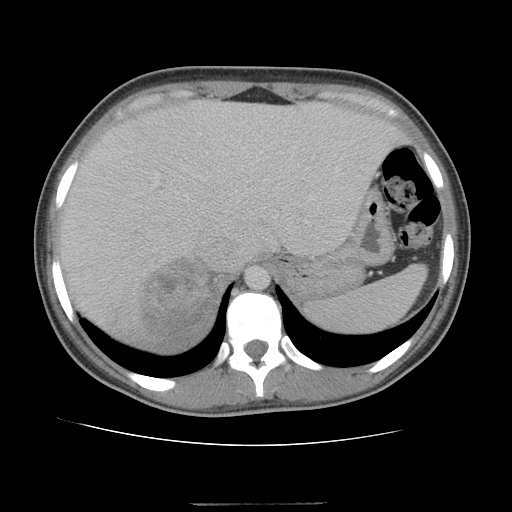
Contrast-enhanced abdominal CT, one axial slice. Slice 83 of 100 in the series (ordered by position). Reconstruction kernel STANDARD. Intravenous contrast given. Soft-tissue window (W 400 / L 40 HU). 5 mm slice thickness. 512 × 512 image matrix, field of view 360 × 360 mm. Female patient, age 21 years. Case-level facts recorded for this patient, not image findings: diagnosis: adrenocortical carcinoma; tumour side: right adrenal; tumour size at pathology: 15.5 cm; Ki-67 index: 26 %; stage (as recorded): 3.
Outlined on this slice (semi-automatic segmentation, software-assisted and operator-edited):
- mass: bounding box <139,259,213,334> (left, top, right, bottom; pixels)